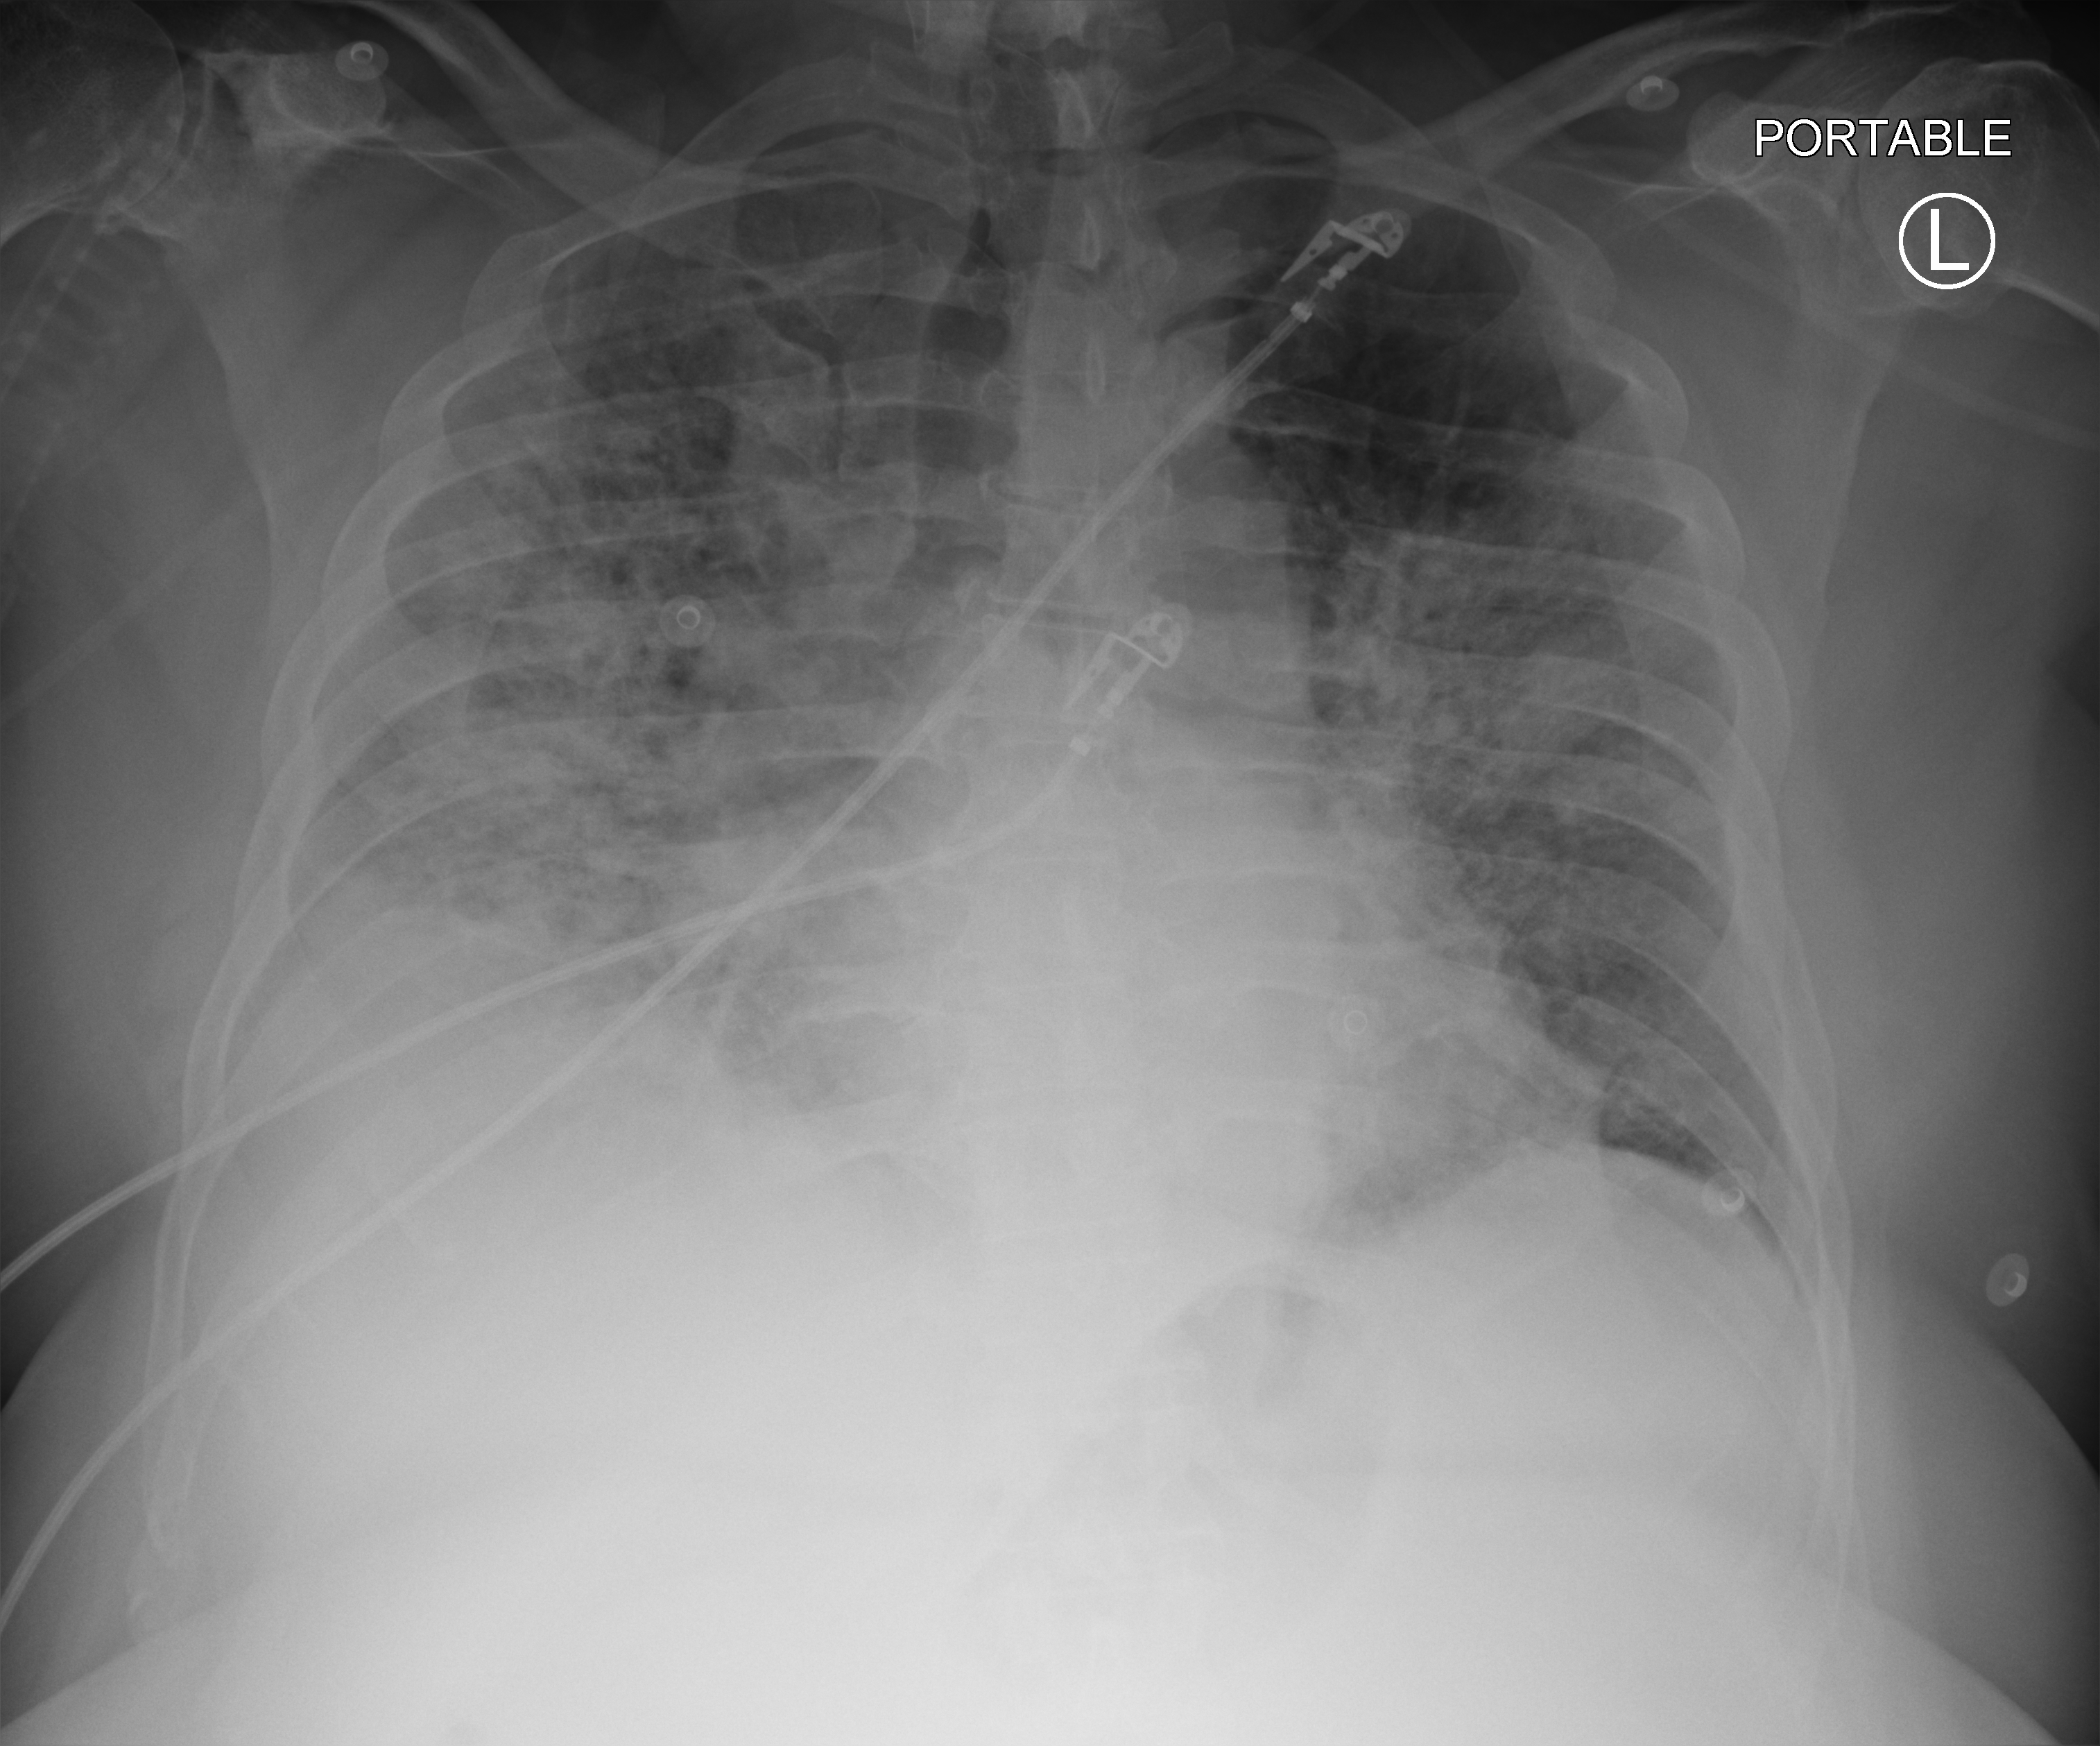
Bedside chest radiograph (computed radiography). Patient hospitalised with COVID-19; male, aged 18–59 years.
Admission-level facts for this patient (not findings on this image; timing relative to this image not recorded): admitted to intensive care during this hospital stay: yes.